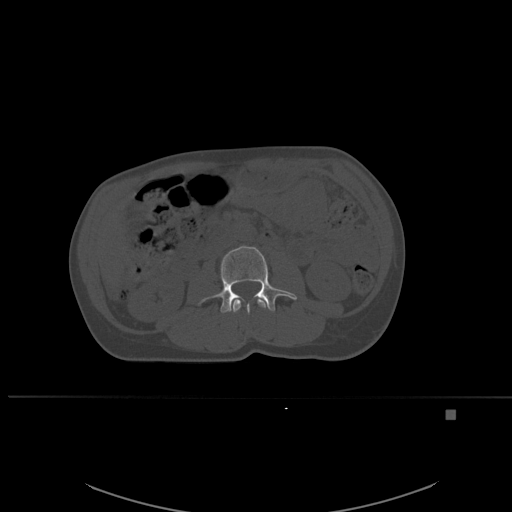
CT including the spine, one axial slice; slice 219 of 537 in the series (ordered by position); bone window (W 1800 / L 400 HU); 1.5 mm slice thickness; 512 × 512 image matrix, field of view 440 × 440 mm. Patient: female, 45 years. From the clinical record (not read from this slice): primary cancer: lung.
Outlined on this slice (semi-automatic segmentation, software-assisted and operator-edited):
- L2 vertebra: bounding box (x1, y1, x2, y2) in pixels: (231, 296, 268, 313)
- L3 vertebra: (200, 245, 297, 313)